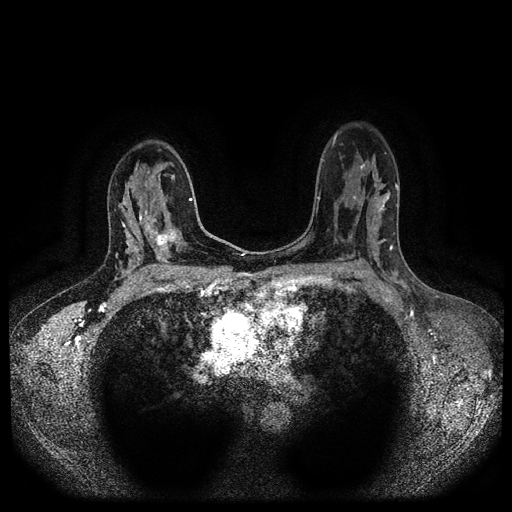
Breast MRI (dynamic contrast-enhanced, multi-phase), one axial slice. Position 66 of 116 along the scan axis. Dynamic contrast-enhanced series, time point 2 of 5 at this slice position (early post-contrast). 1.5 T. TE 2.6 ms, TR 5.4 ms. 2 mm slice thickness. 512 × 512 image matrix, field of view 340 × 340 mm. Female patient, age 47 years.
Outlined on this slice (semi-automatically segmented with operator editing):
- breast lesion (labelled 'tumour' in the annotation; benign lesions carry a separate 'benign' label): bounding box <142,208,180,261> (left, top, right, bottom; pixels)